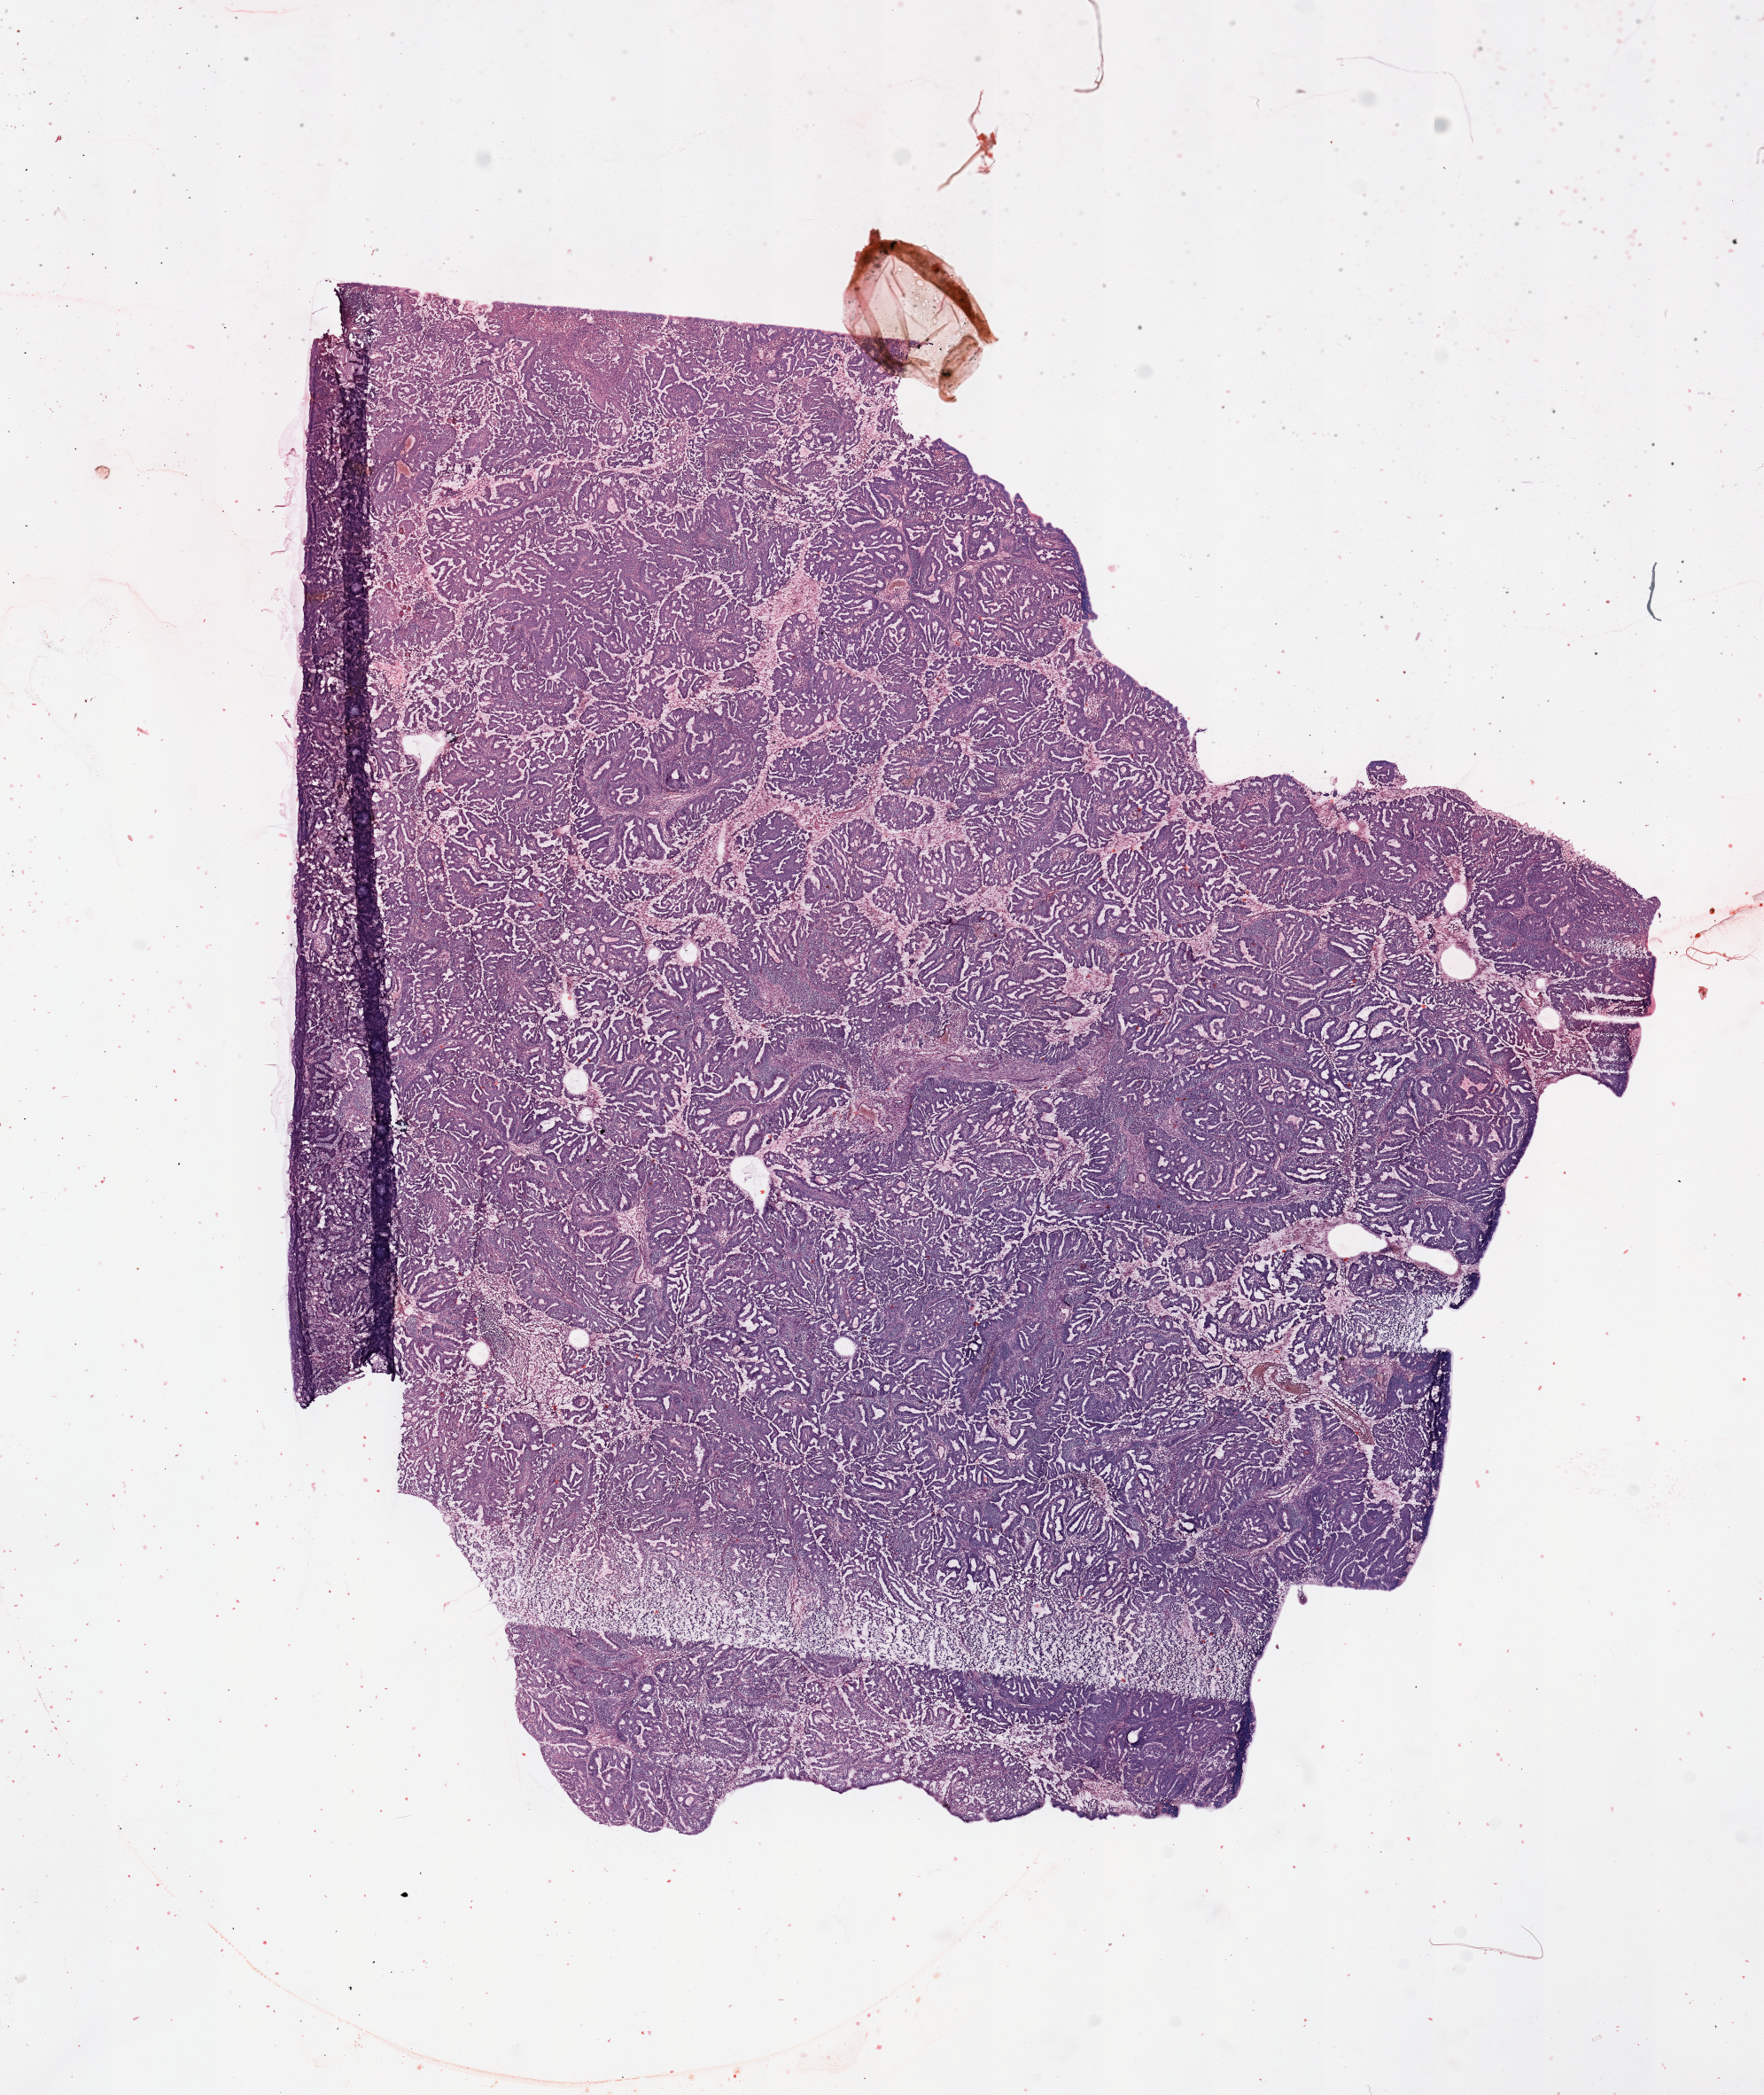
H&E-stained whole-slide image, shown as a low-resolution overview of the whole scanned area (about 15.8 x 18.7 mm). Tumour tissue sample, uterus. 59-year-old female patient.
Histologic diagnosis: Endometrioid adenocarcinoma, NOS.